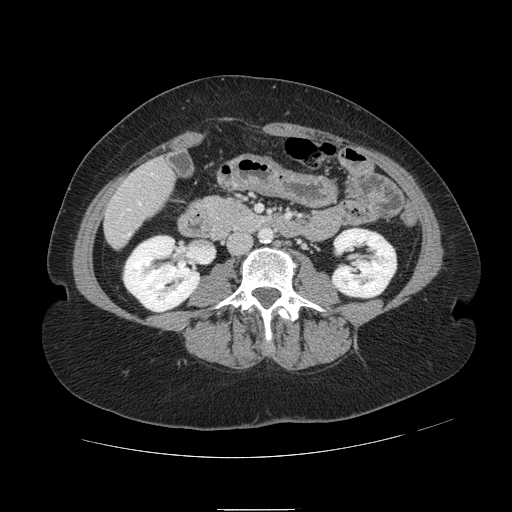
Contrast-enhanced abdominal CT, one axial slice. Slice 17 of 121 in the series (ordered by position). 120 kVp. Intravenous contrast given. Soft-tissue window (W 400 / L 40 HU). 2.5 mm slice thickness. 512 × 512 image matrix. Female patient, age 52 years. Case-level facts recorded for this patient, not image findings: diagnosis: colorectal cancer liver metastases, imaged before liver resection; multiple liver metastases: yes; largest metastasis: 6.3 cm.
Annotated regions visible in this slice (manually delineated by an expert):
- hepatic veins: bounding box [x1, y1, x2, y2] px = [127, 174, 153, 235]
- liver: [106, 162, 172, 245]
- portal vein (with intrahepatic branches): [128, 209, 130, 211]